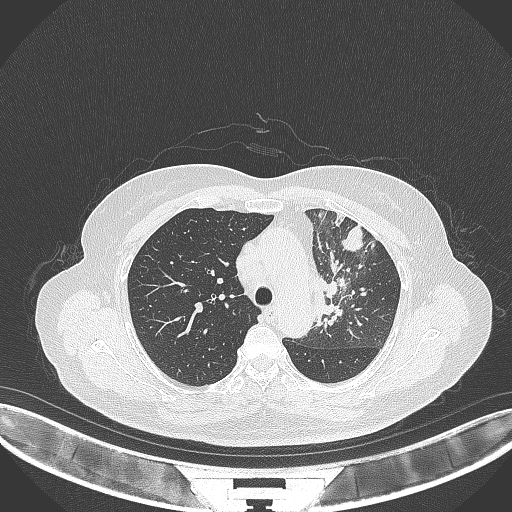
Chest CT, one axial slice; position 244 of 382 along the scan axis; reconstruction kernel B70f; lung window (W 1500 / L -600 HU); 1 mm slice thickness; 512 × 512 image matrix. Patient: female, 64 years. Case-level facts recorded for this patient, not image findings: clinical TNM (as recorded): T2a N2 M0.
Annotated regions visible in this slice (rectangle marked by the reading radiologist):
- lung tumour (recorded histology: adenocarcinoma): box from (x=312, y=265) to (x=348, y=333) px
- lung tumour (recorded histology: adenocarcinoma): (x=337, y=219)–(x=369, y=257)